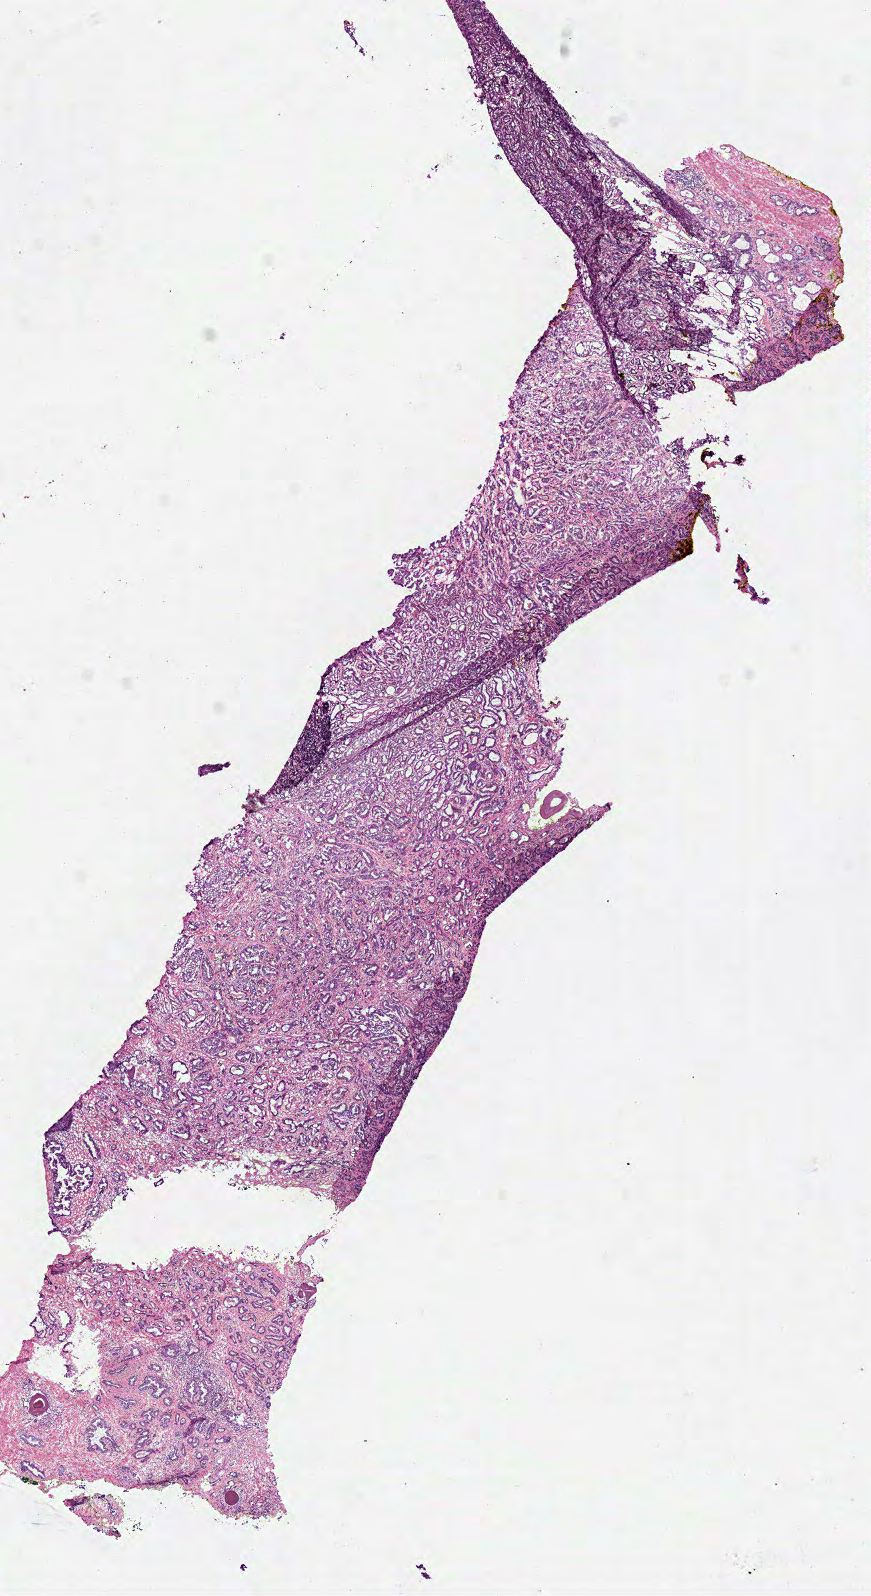
Whole-slide histology image, Hematoxylin and eosin (H&E) stained, low-resolution overview of the scanned area, about 6.9 x 12.6 mm (from a 40x scan), frozen section from the top of the tissue portion, primary tumour sample from the prostate. Patient: male, age at initial diagnosis 61 years. Gleason score: 7 (3+4). Slide review estimates, as recorded: tumour cells 85%, tumour nuclei 90%, normal cells 3%, stromal cells 12%, necrosis 0%. Infiltration values recorded for this section: lymphocyte infiltration 2%, monocyte infiltration 0%, neutrophil infiltration 0%.
Pathologic diagnosis: Acinar cell carcinoma (prostate gland). Laterality: bilateral.